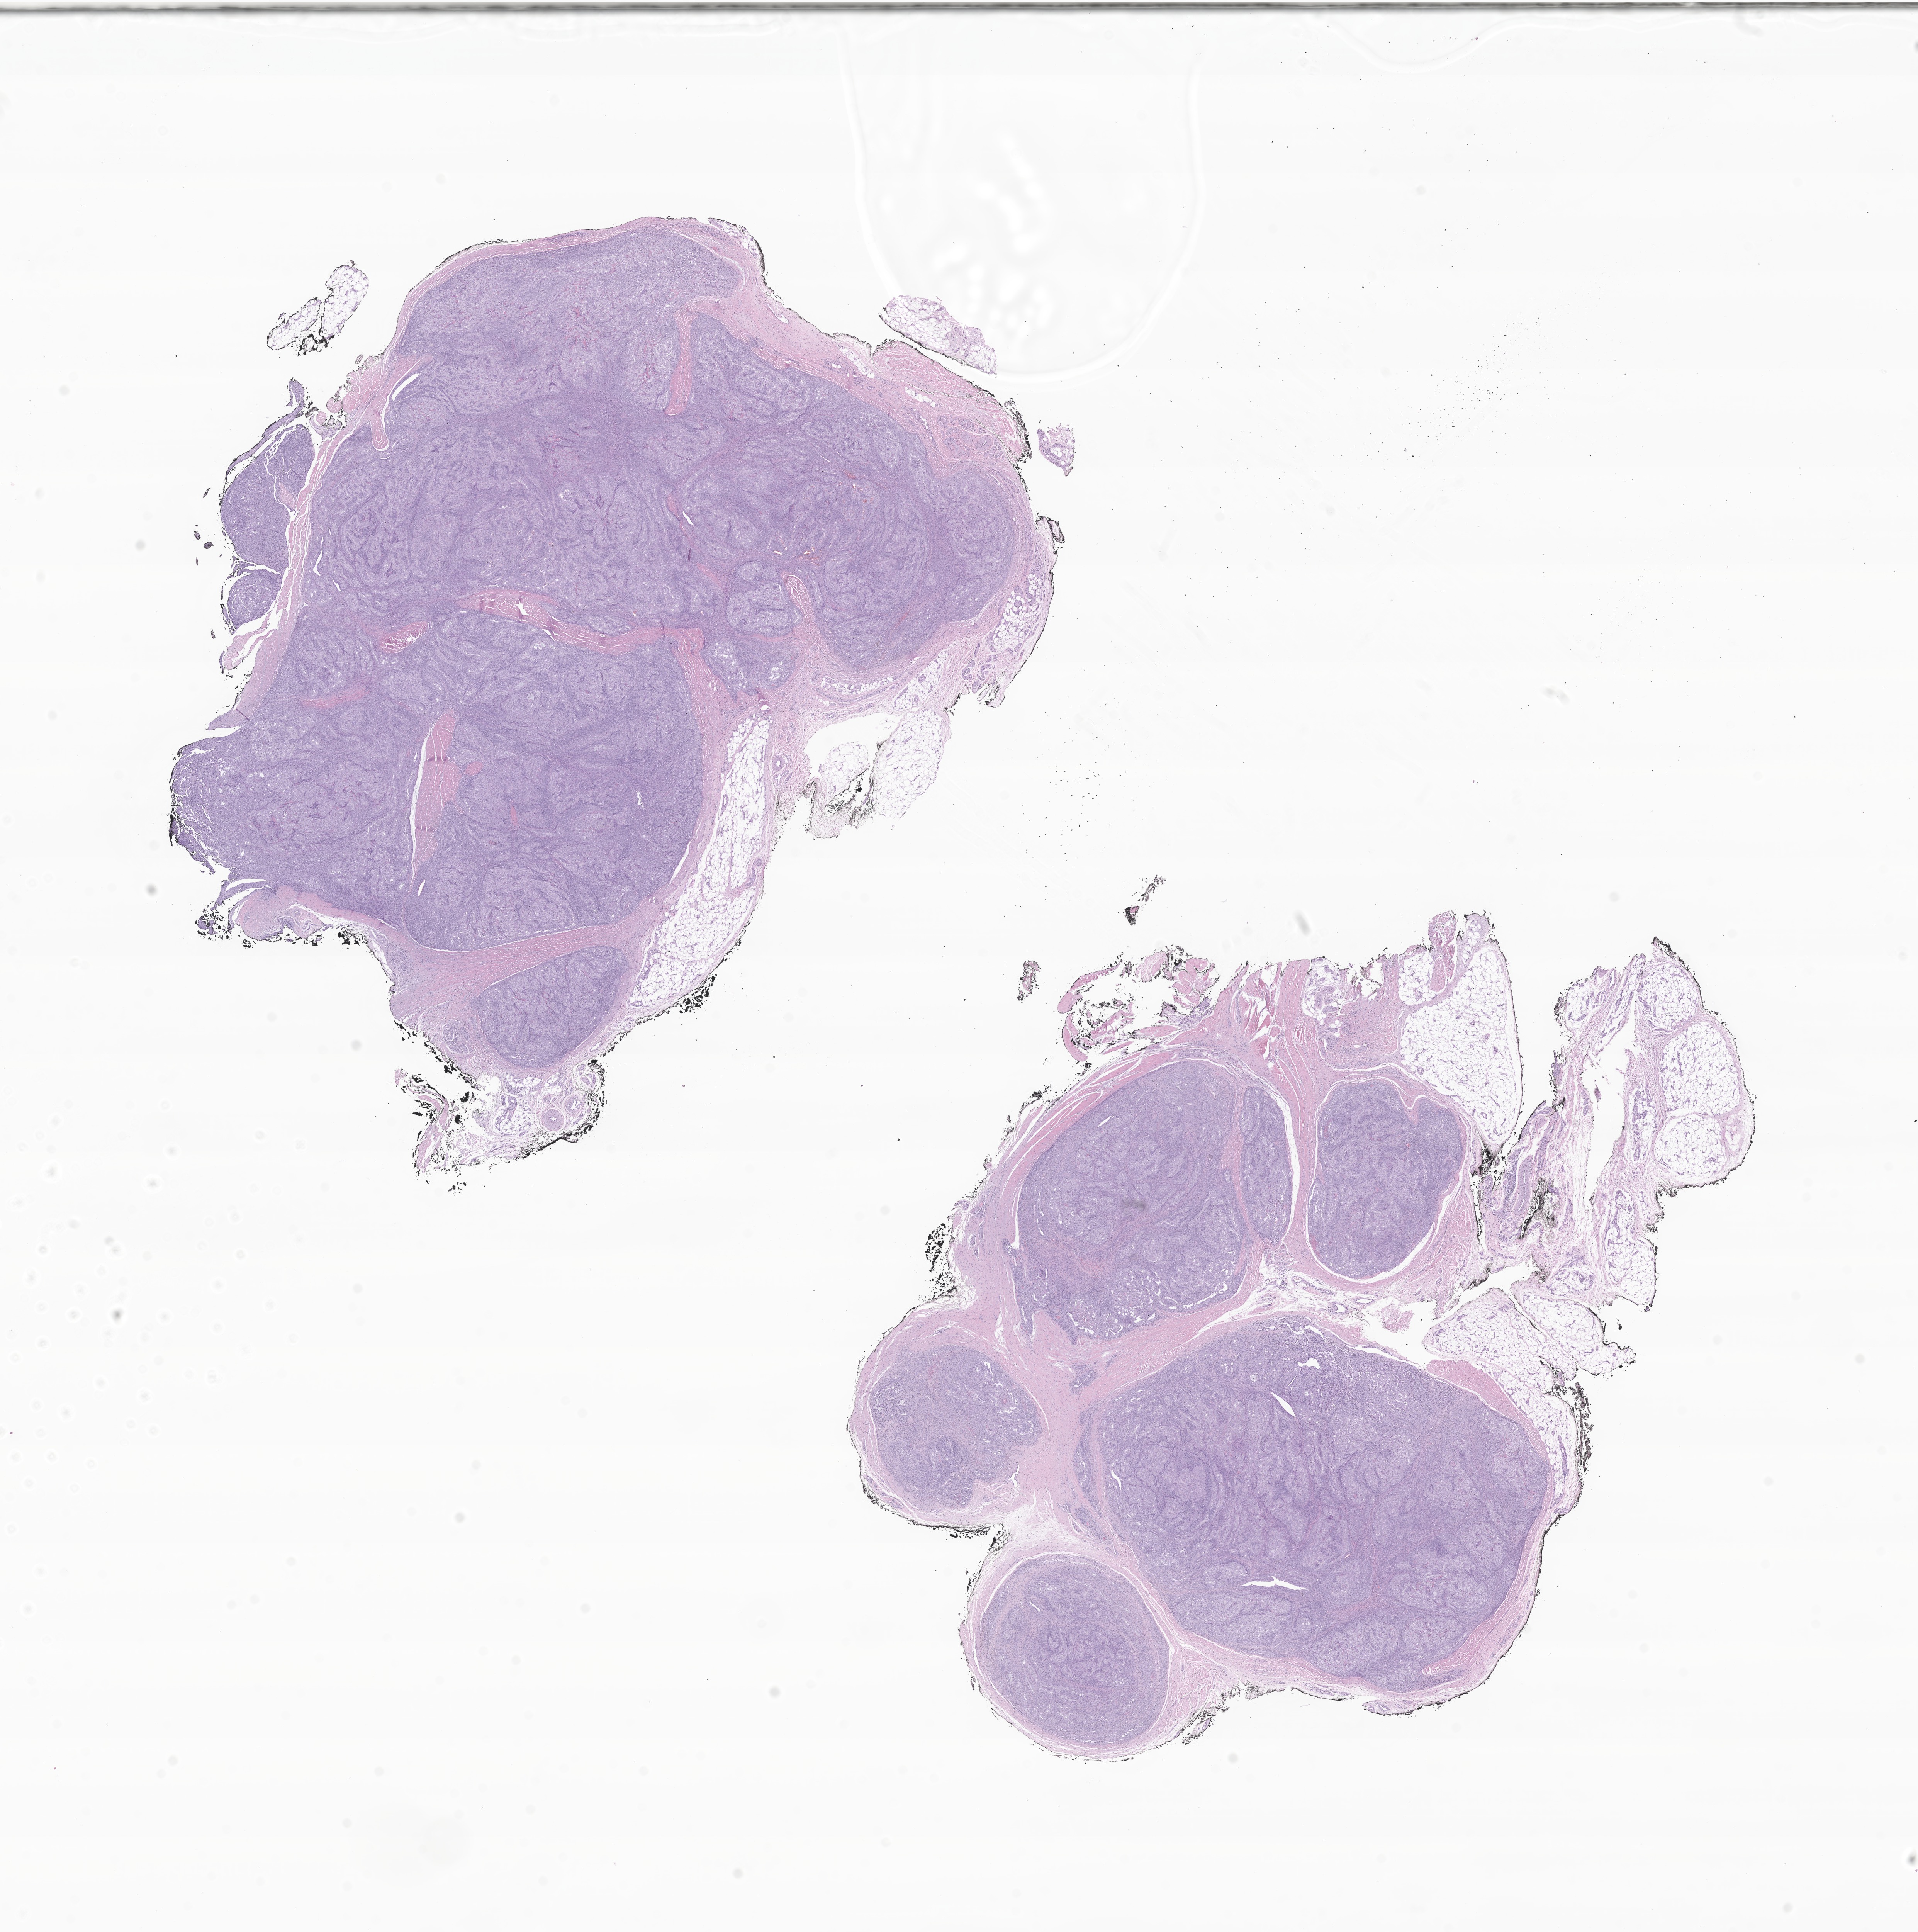
Haematoxylin and eosin whole-slide image of tumor tissue from the soft tissue of lower extremity, a low-resolution overview of the entire scanned area, about 20.9 x 21.1 mm; FFPE section. Patient: female, age 140 months (11 years 8 months).
Diagnosis: Synovial sarcoma, biphasic.